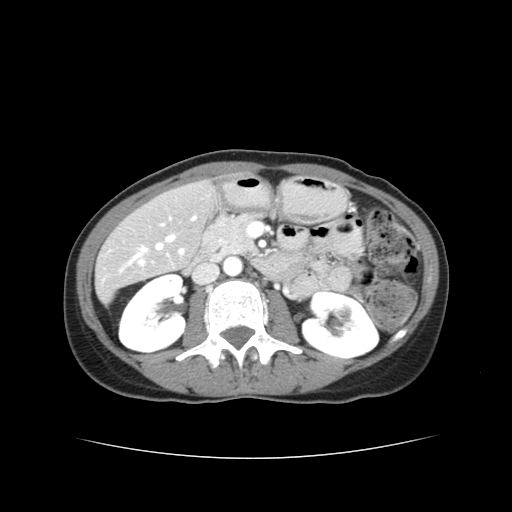
Contrast-enhanced abdominal CT, one axial slice; position 14 of 38 along the scan axis; reconstruction kernel STANDARD; intravenous contrast given; soft-tissue window (W 400 / L 40 HU); 5 mm slice thickness; 512 × 512 image matrix, field of view 340 × 340 mm. Female patient, age 54 years. From the clinical record (not read from this slice): diagnosis: colorectal cancer liver metastases, imaged before liver resection; multiple liver metastases: yes; largest metastasis: 1.1 cm; disease in both lobes: yes.
Outlined on this slice (outlined manually by an expert reader):
- hepatic veins: bounding box <143,236,174,252> (left, top, right, bottom; pixels)
- liver: <96,183,209,298>
- portal vein (with intrahepatic branches): <132,217,196,265>